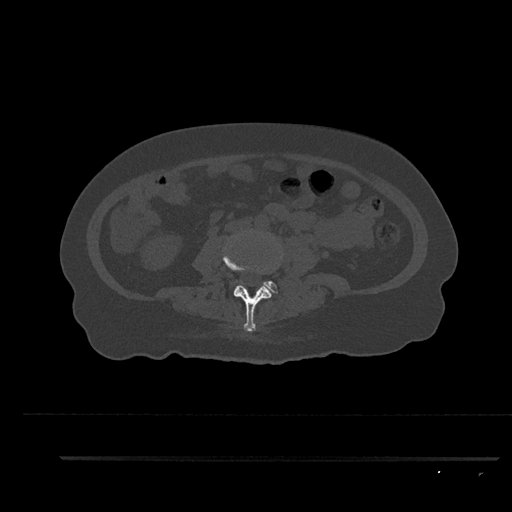
CT including the spine, one axial slice; slice 63 of 797 in the series (ordered by position); 120 kVp; bone window (W 1800 / L 400 HU); 512 × 512 image matrix, field of view 408 × 408 mm. Patient: female, 44 years. From the clinical record (not read from this slice): primary cancer: renal; vertebrae with lytic lesions (as recorded): L1.
Annotated regions visible in this slice (semi-automatic segmentation, software-assisted and operator-edited):
- L3 vertebra: box from (x=223, y=247) to (x=272, y=332) px
- L4 vertebra: (x=263, y=281)–(x=278, y=294)